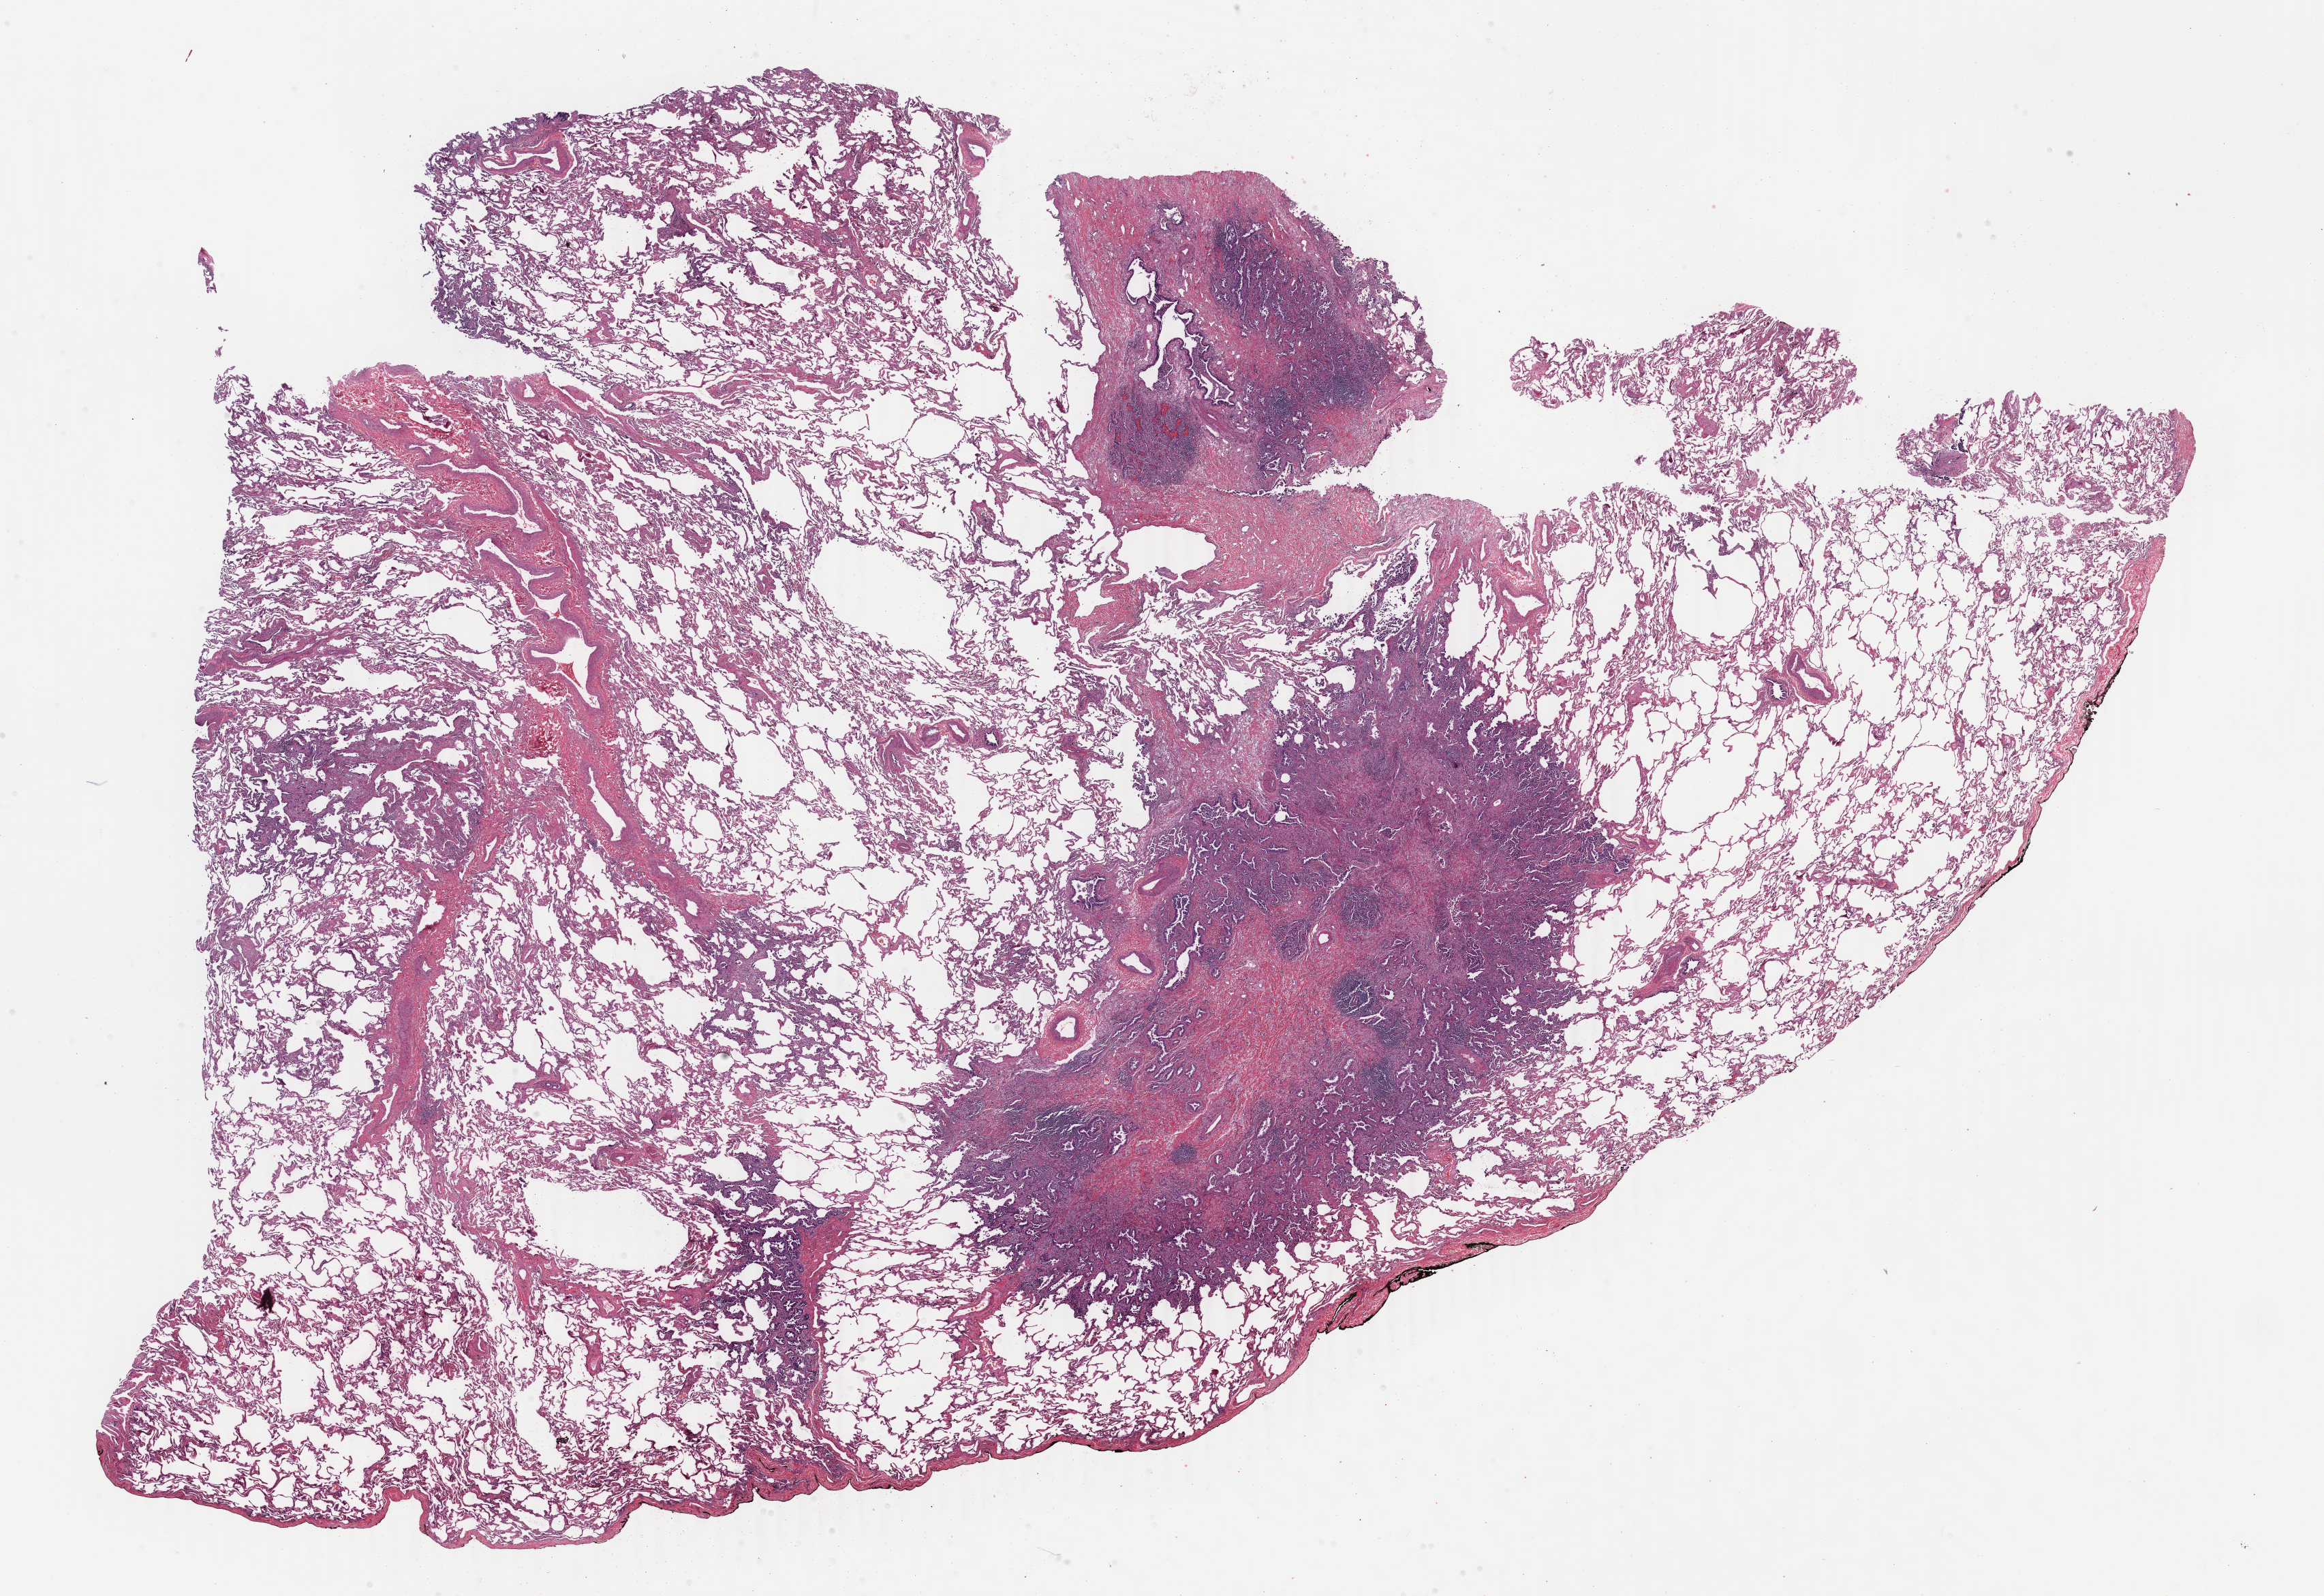
Whole-slide histology image, H&E, whole scanned area (about 27.1 x 18.6 mm, acquisition: 40x scan) shown as a low-resolution overview. FFPE section. Primary tumour sample from the lung. Patient: female, age at initial diagnosis 60 years.
Diagnosis: Adenocarcinoma with mixed subtypes.